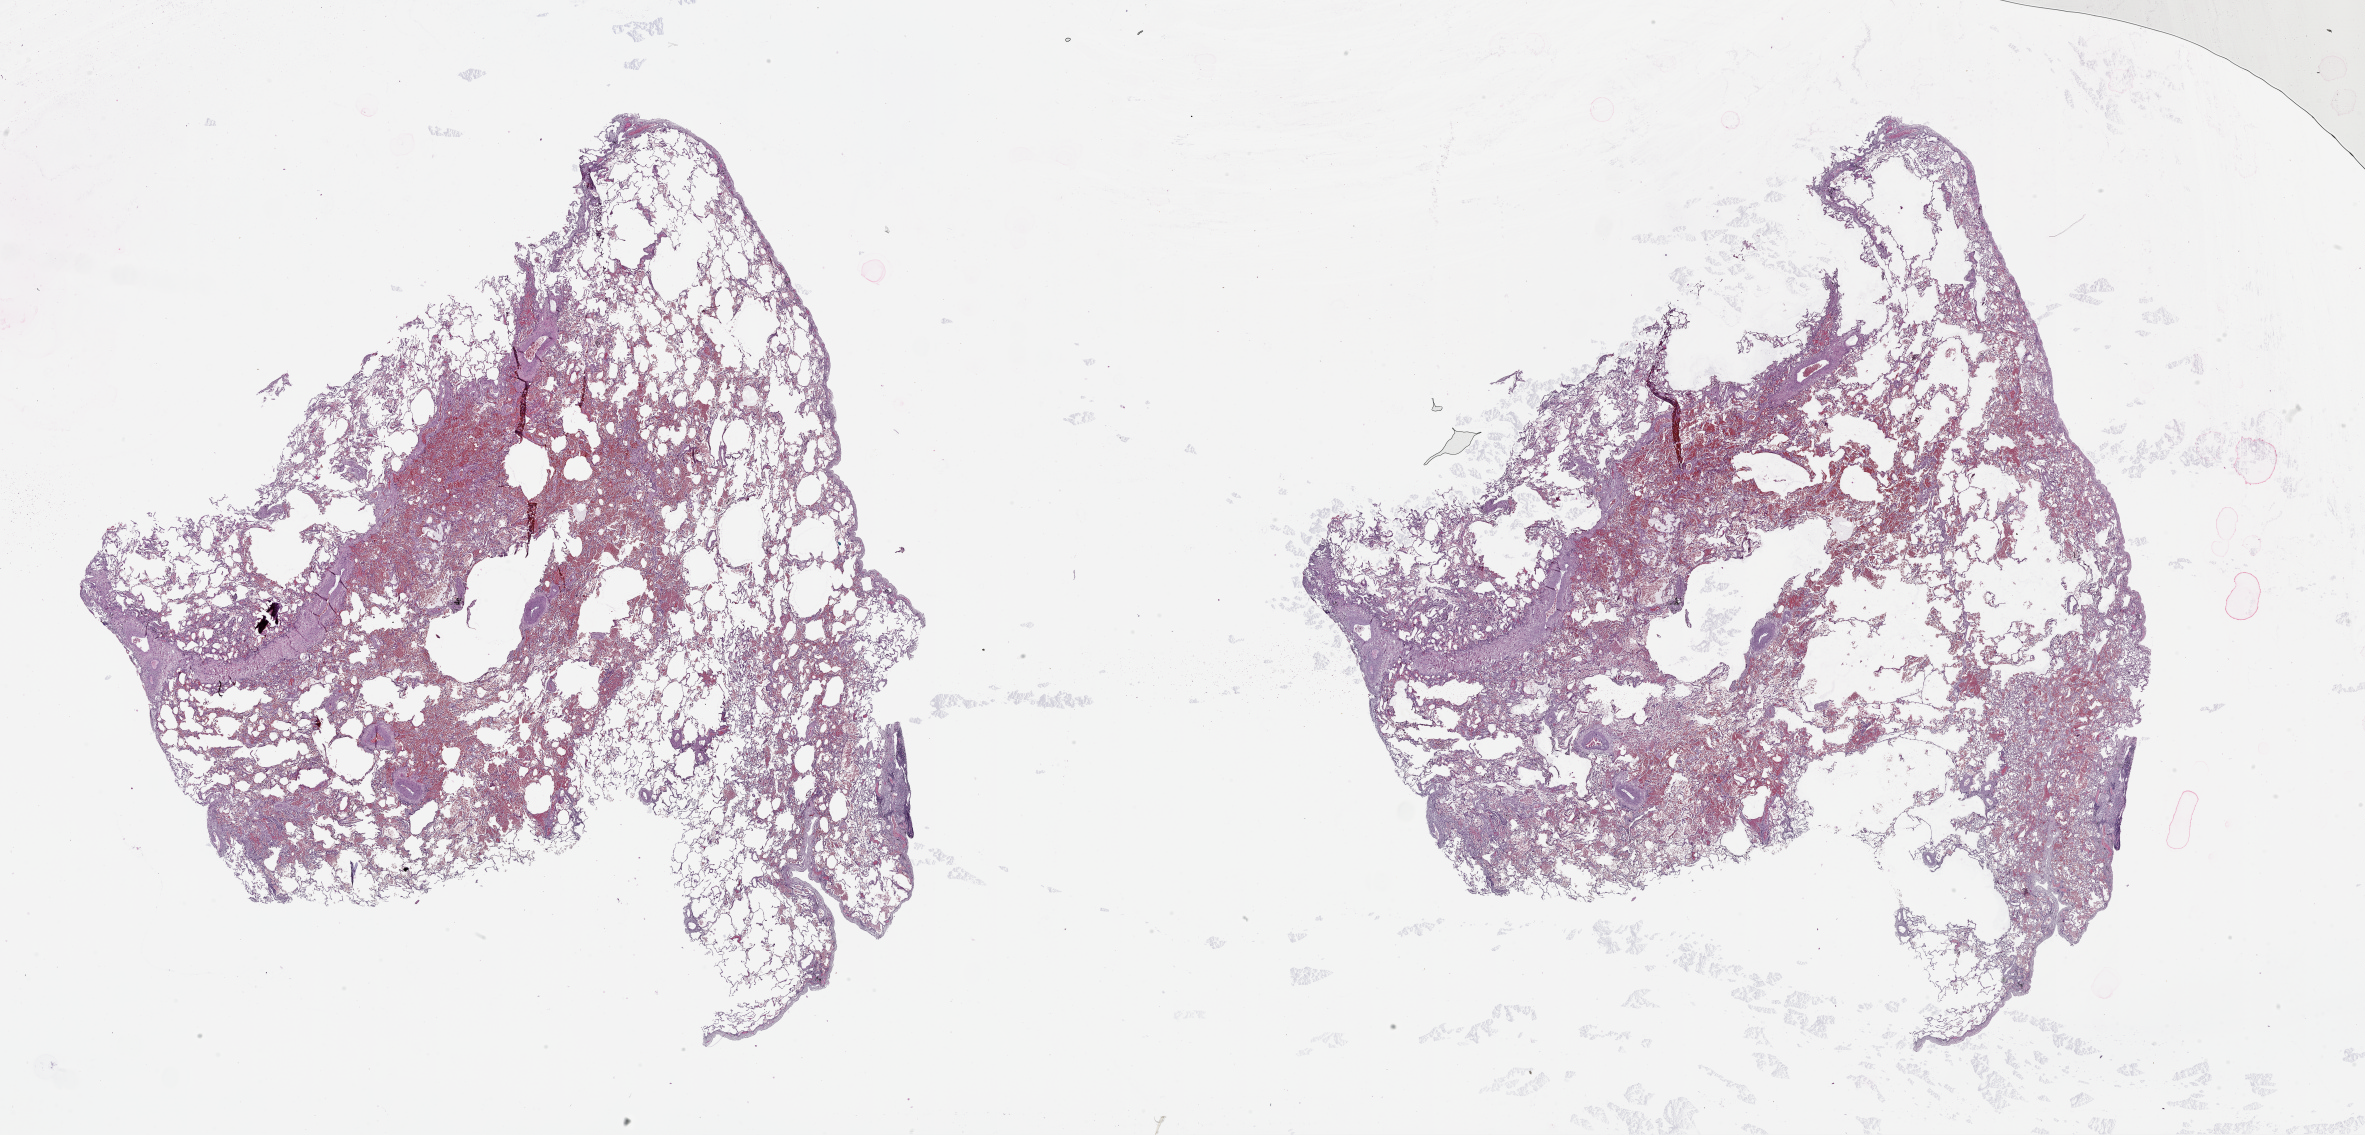
Hematoxylin and eosin (H&E) stained whole-slide image — whole scanned area (about 38.1 x 18.3 mm, slide scanned at 20x) shown as a low-resolution overview, lung, normal (non-tumour) tissue. Patient: male, age 65 years.
This section: normal (non-tumour) tissue from the same patient. Patient diagnosis (cohort enrolment): squamous cell carcinoma (lung).